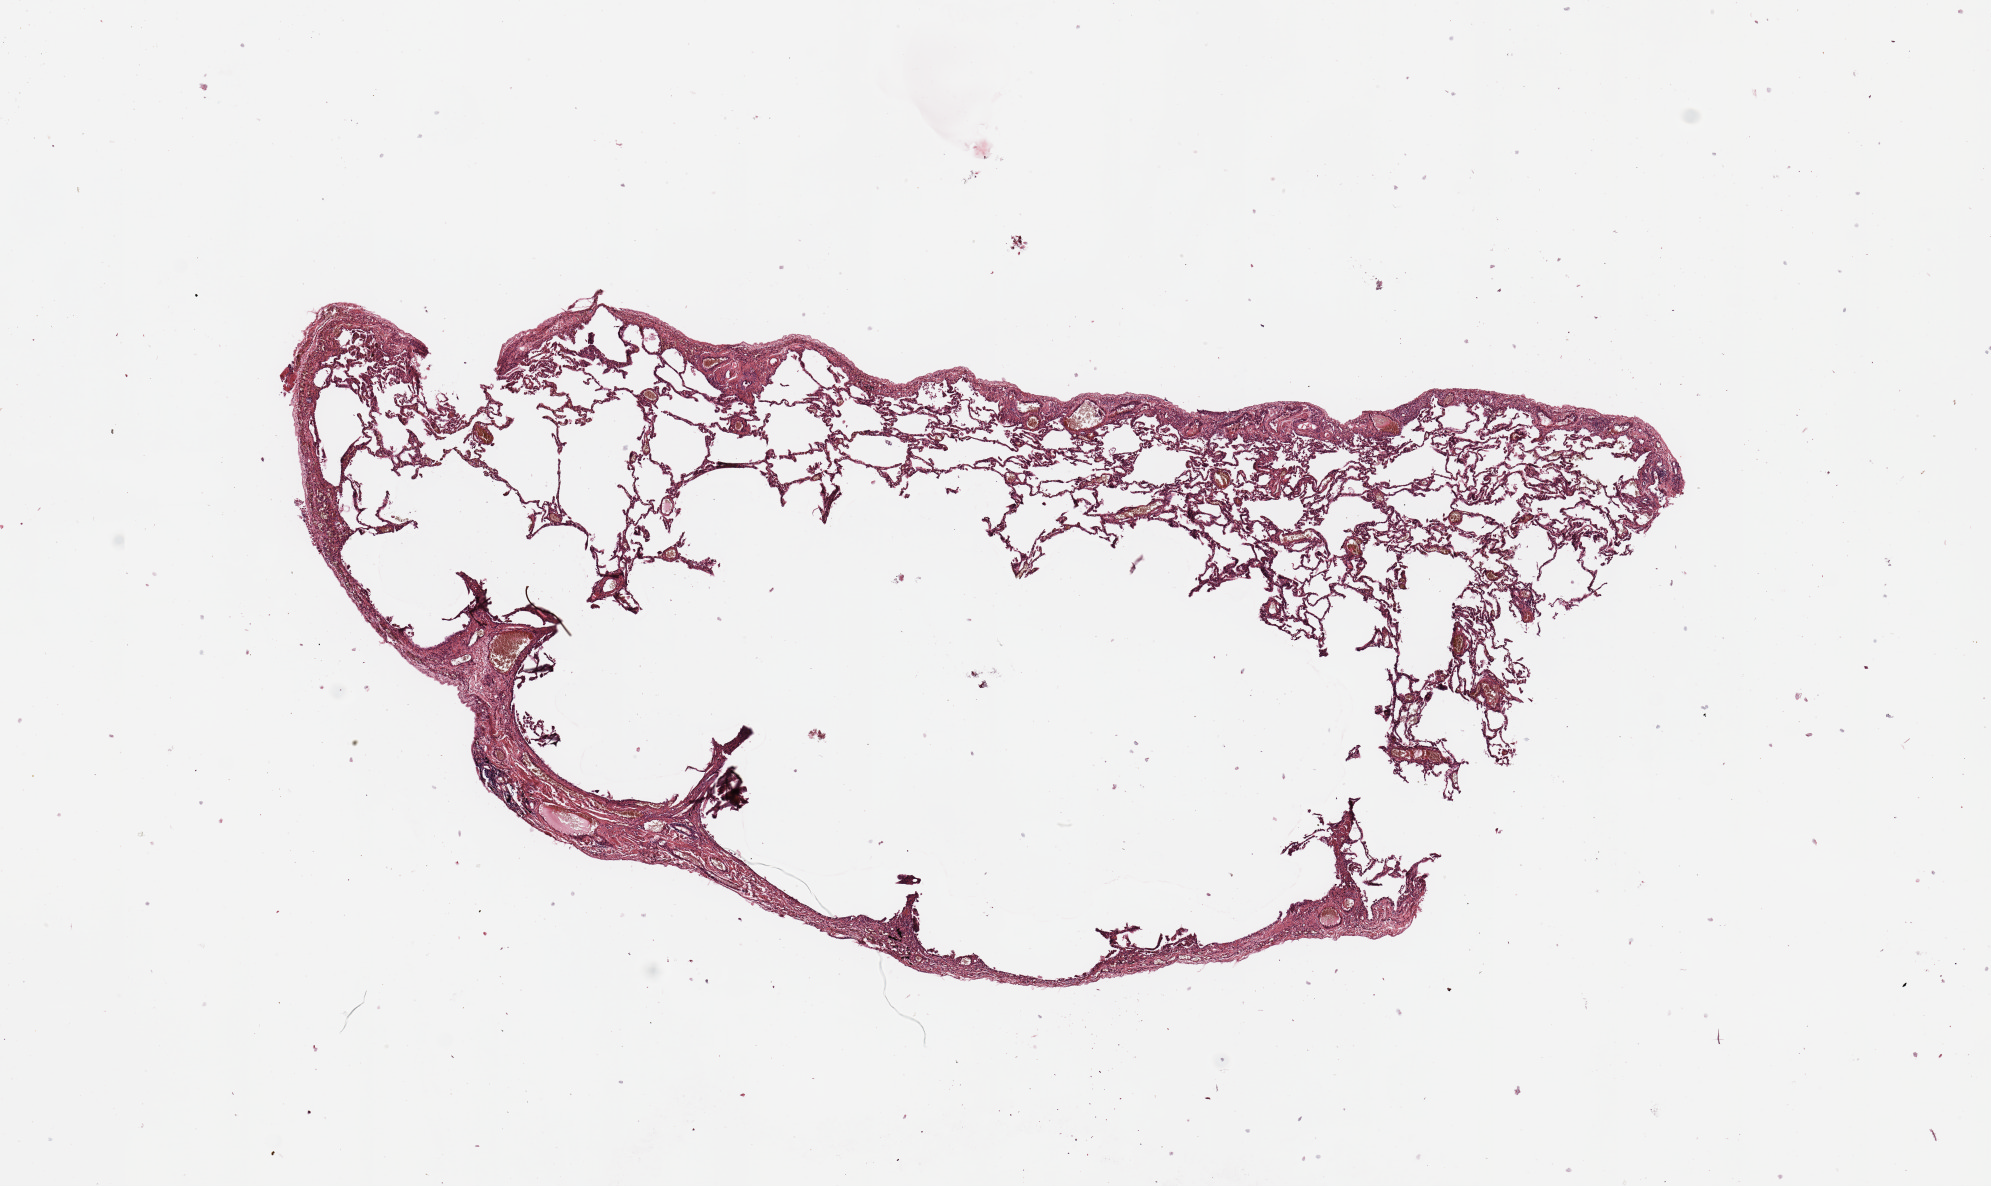
H&E whole-slide image, whole scanned area (about 15.8 x 9.4 mm, from a 20x scan) shown as a low-resolution overview. Normal (non-tumour) tissue sample, sampled site: lung. Patient: male, age 70 years.
This section: normal (non-tumour) tissue from the same patient. Patient diagnosis: Squamous cell carcinoma, NOS.